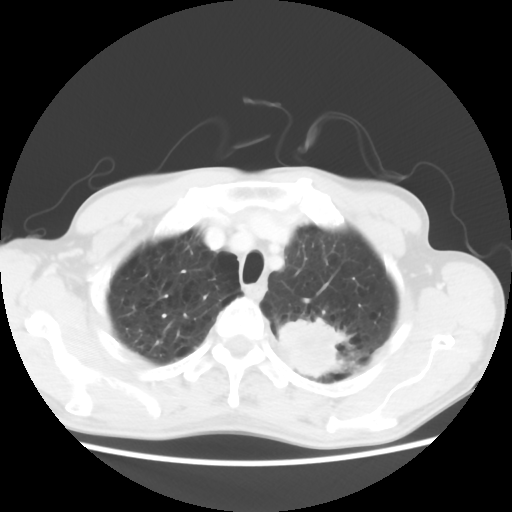
Chest CT, one axial slice. Position 54 of 64 along the scan axis. Reconstruction kernel STANDARD. 120 kVp. Lung window (W 1500 / L -600 HU). 512 × 512 image matrix. Patient: male, 63 years. Case-level facts recorded for this patient, not image findings: clinical TNM (as recorded): T2 N0 M0.
Structures marked on this image (rectangle marked by the reading radiologist):
- lung tumour (recorded histology: adenocarcinoma): bounding box (x1, y1, x2, y2) in pixels: (275, 310, 342, 383)